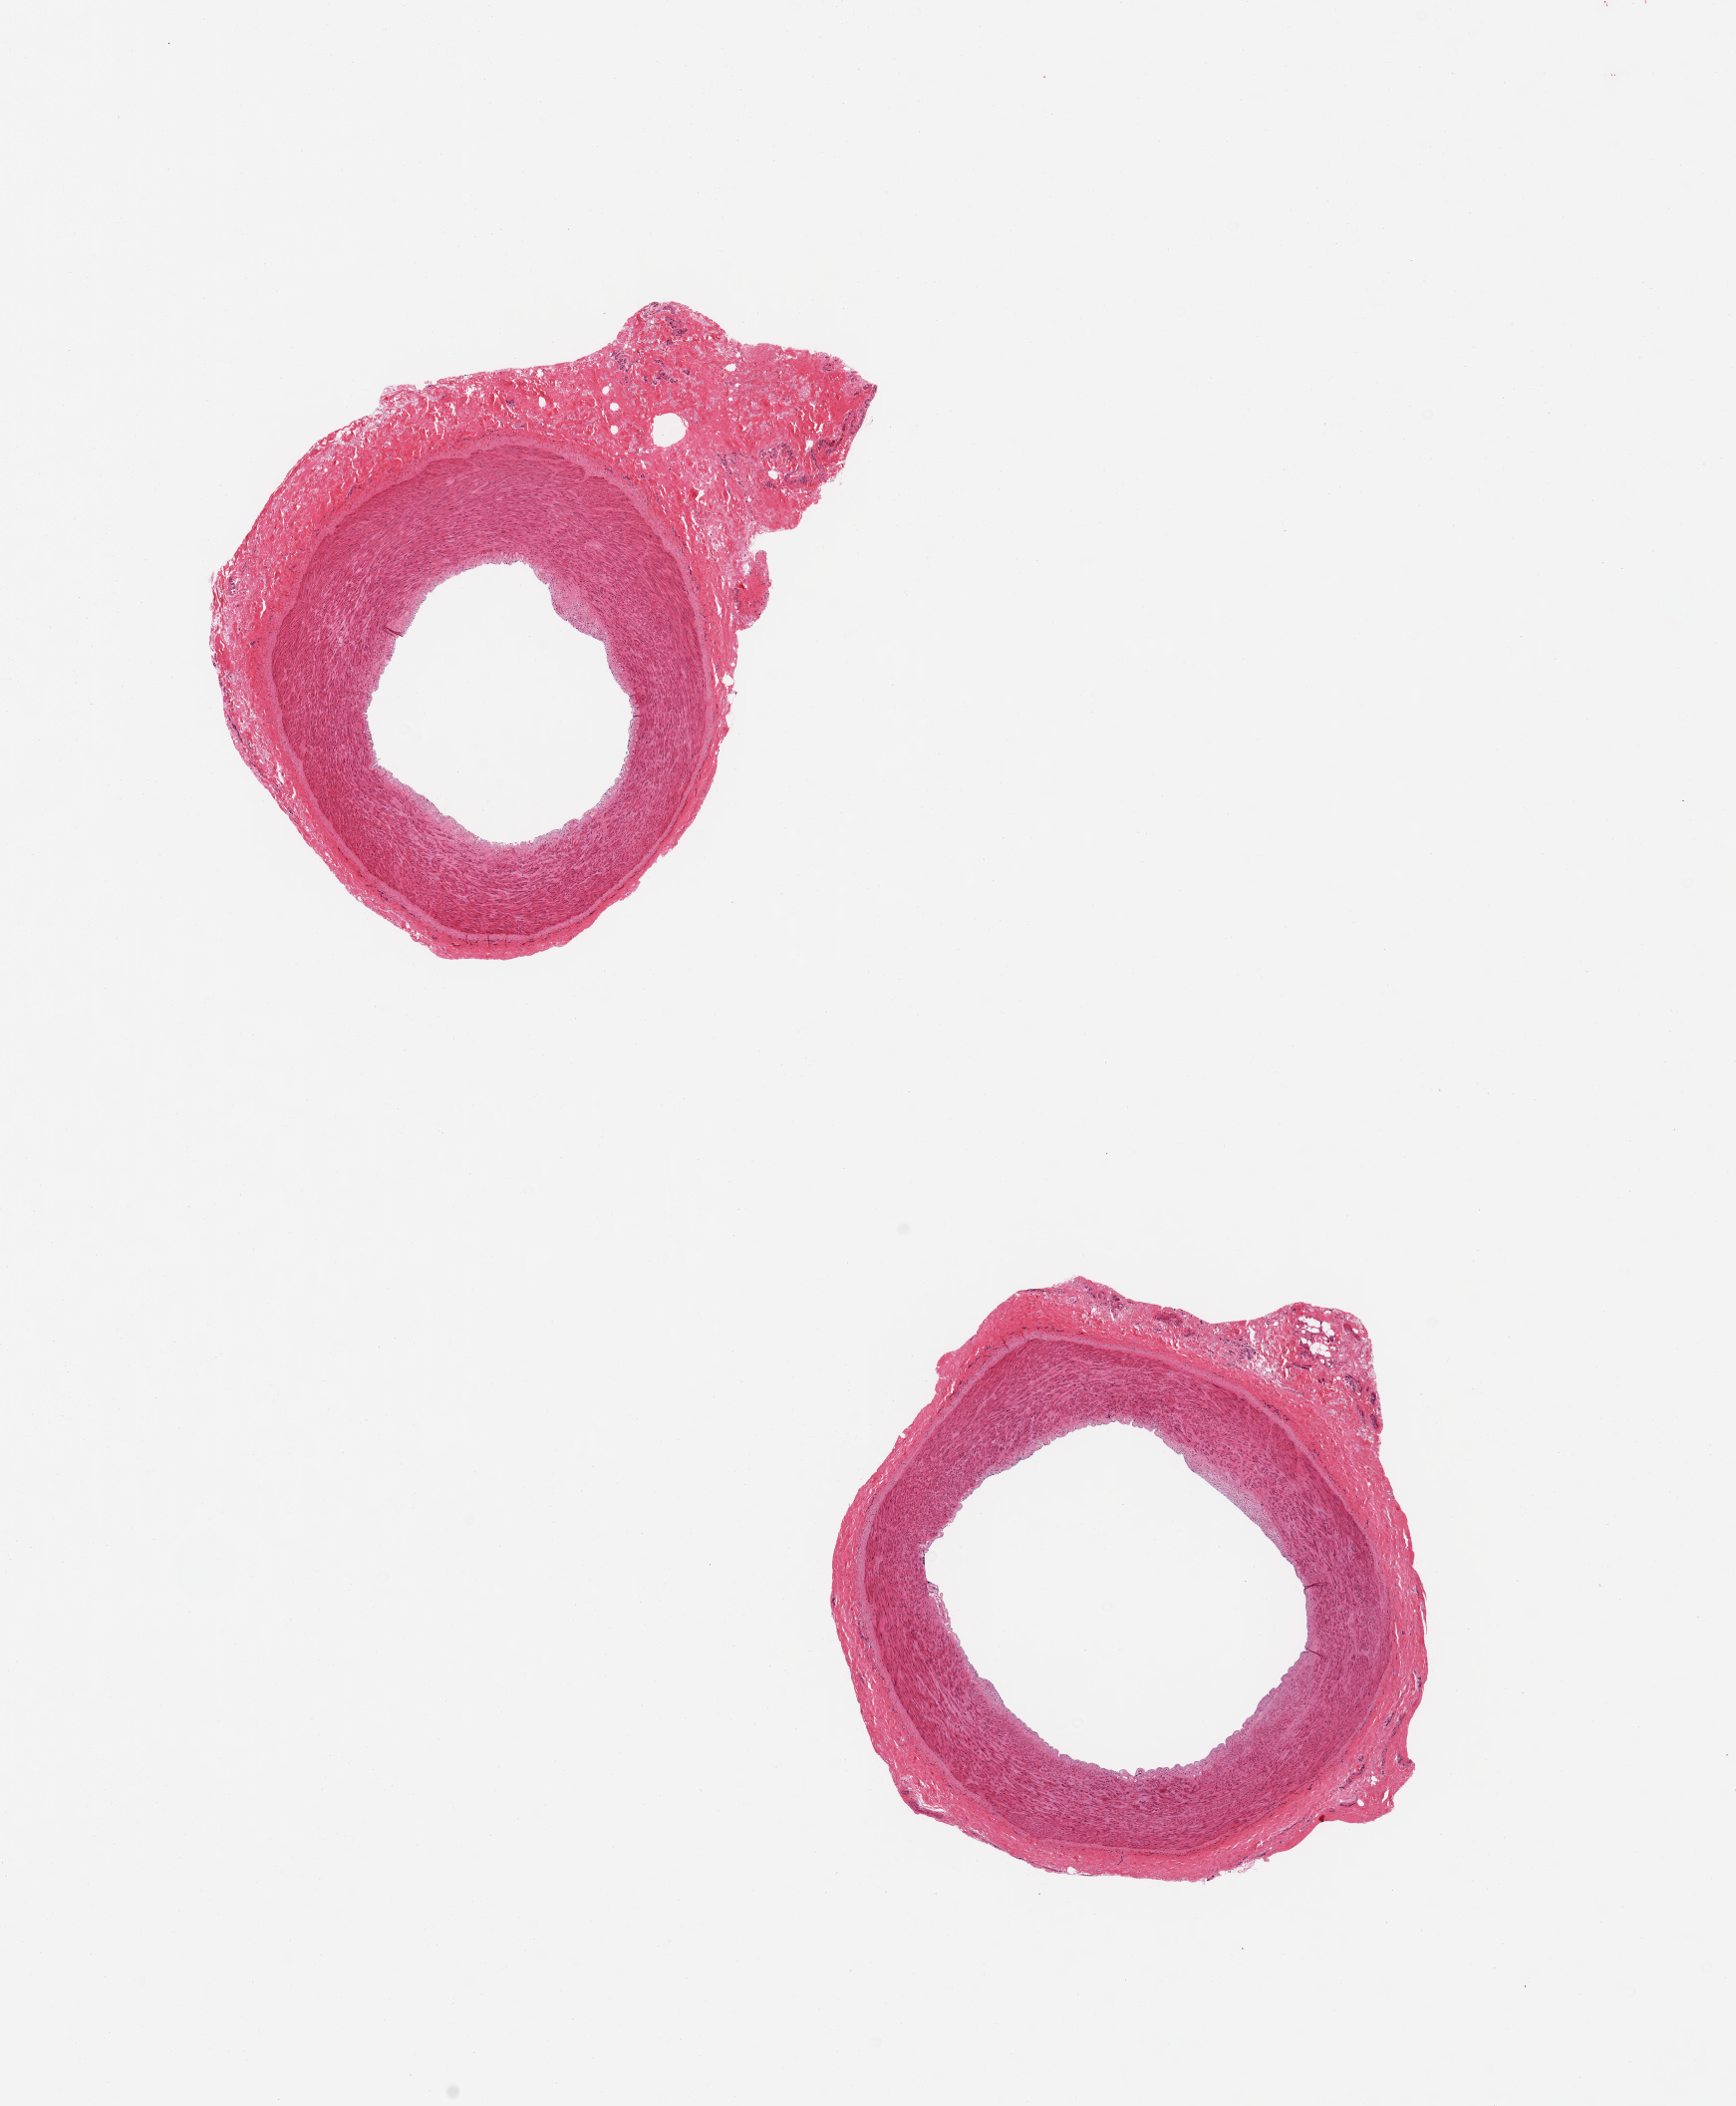
Haematoxylin and eosin whole-slide image, shown as a low-resolution overview of the whole scanned area (about 13.8 x 16.7 mm, acquisition: 20x scan); PAXgene-fixed, paraffin-embedded tissue; section of tibial artery (target tissue); donor tissue sample. Donor sex: male.
Pathologist's review note for this sample: 2 pieces, trace atherosis; adherent 2 mm nubbin fibrous tissue, otherwise clean.